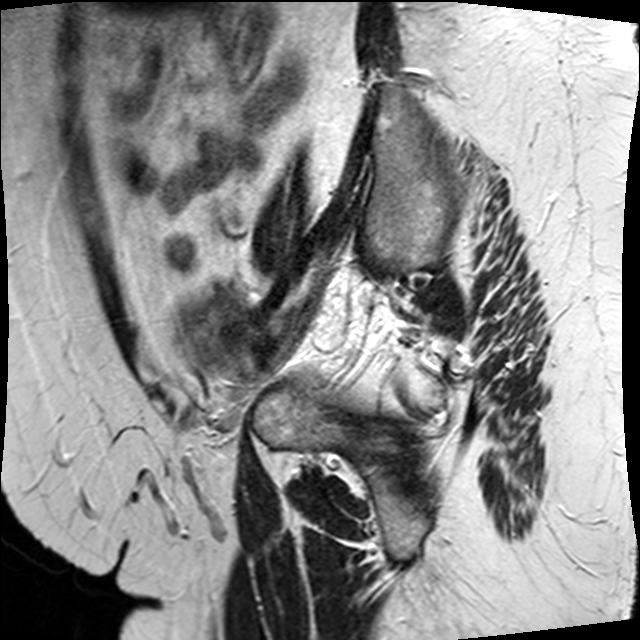
Pelvic MRI for cervical cancer, one sagittal slice. Position 6 of 34 along the scan axis. T2-weighted. 1.5 T. TE 89 ms, TR 3320 ms. 4 mm slice thickness. 640 × 640 image matrix. Patient: female, 50 years.
Outlined on this slice (outlined manually by an expert reader):
- uterus and cervix: bounding box [x1, y1, x2, y2] px = [172, 287, 266, 377]